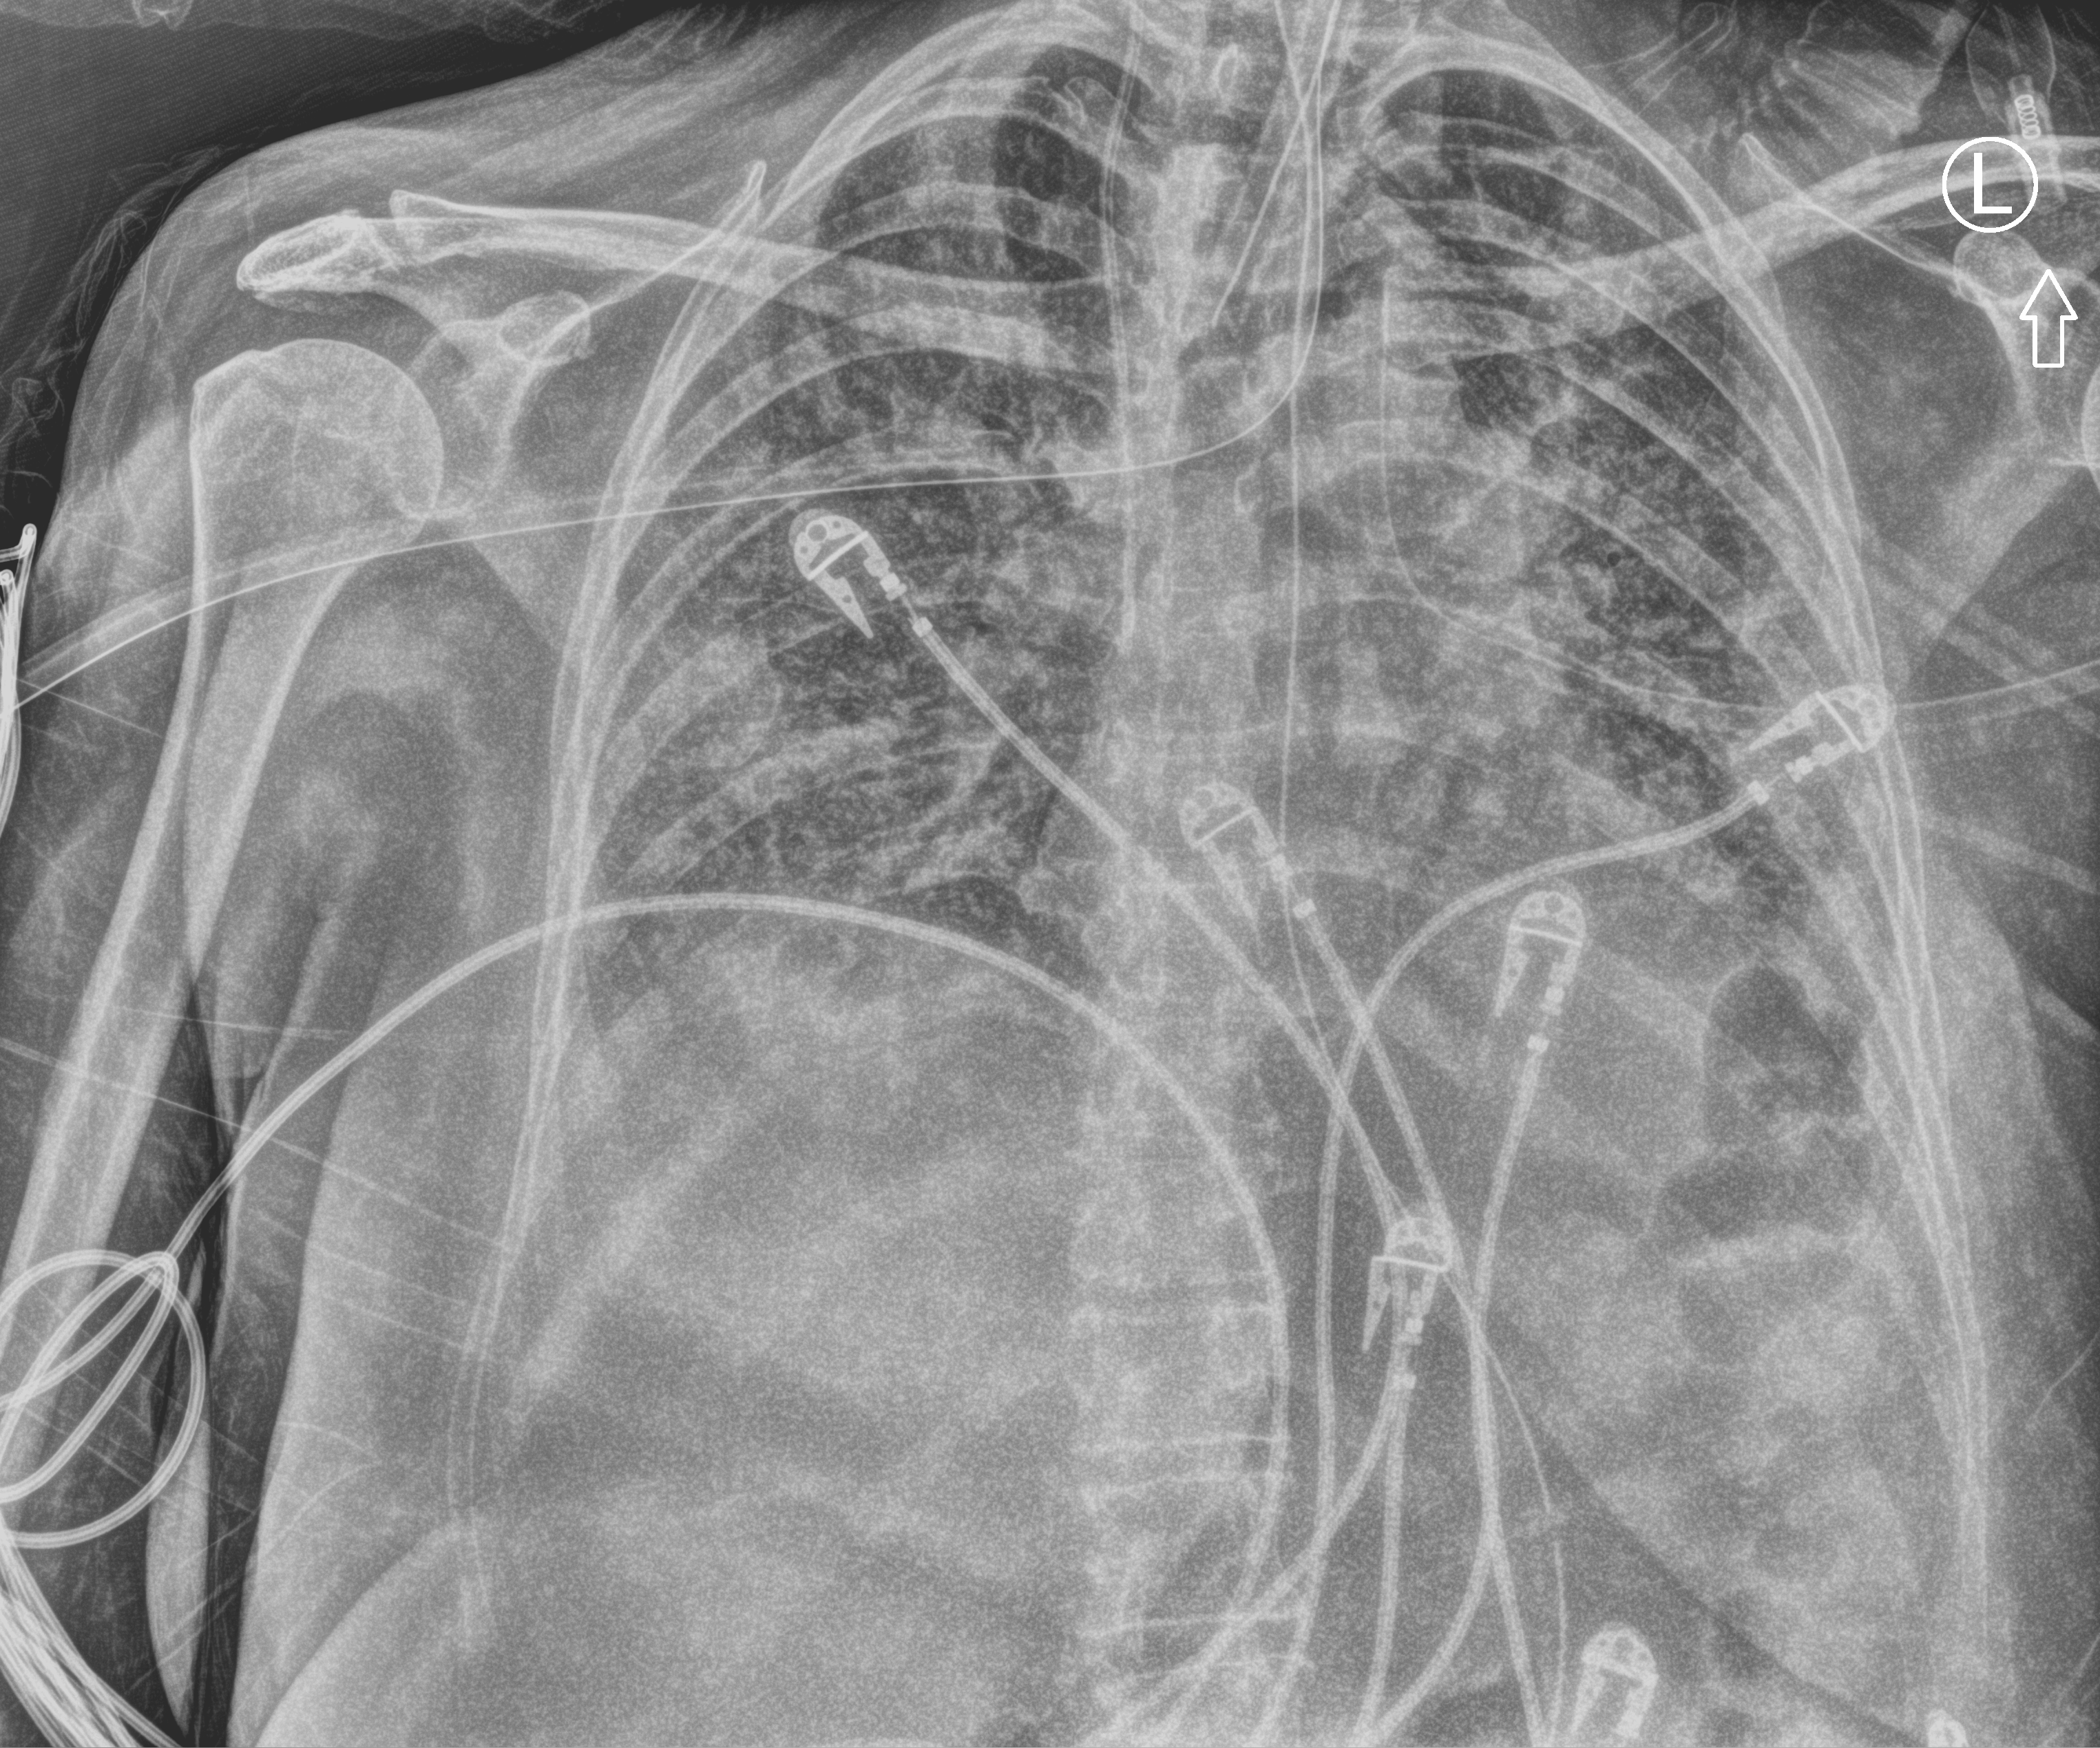
Chest X-ray (portable), anteroposterior (AP) projection. Female patient hospitalised with COVID-19, age 60–74 years.
Admission-level facts for this patient (not findings on this image; timing relative to this image not recorded):
- hypertension (admission record): yes